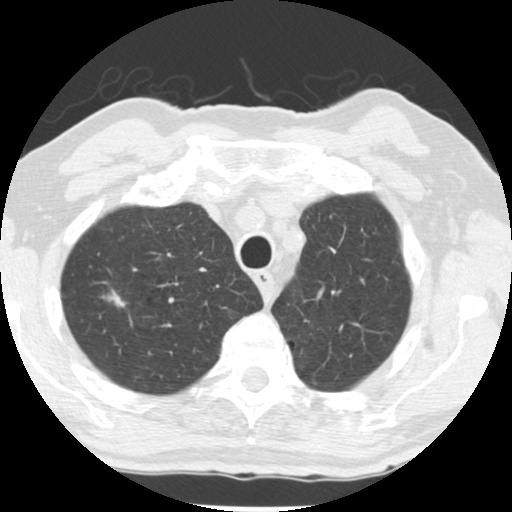
Low-dose screening chest CT, one axial slice; position 209 of 252 along the scan axis; 120 kVp; lung window (W 1500 / L -600 HU); 2.5 mm slice thickness; 512 × 512 image matrix.
Structures marked on this image (outlined manually by an expert reader):
- lesion 1 (tumor, upper lobe of right lung): box from (x=104, y=289) to (x=126, y=308) px